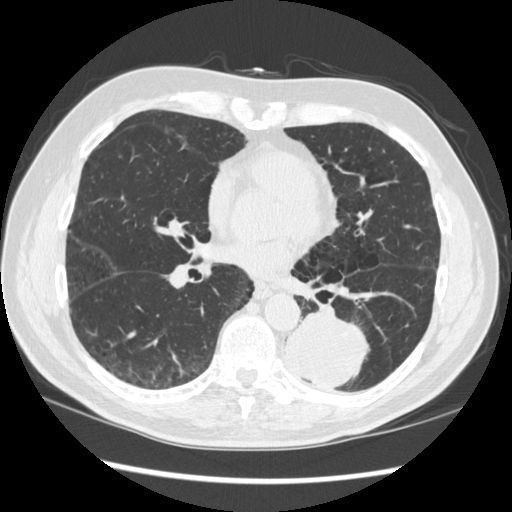
Chest CT (low-dose screening protocol), one axial image; first (baseline) screen; lung window (W 1500 / L -600 HU); 1.25 mm slice thickness; slice 150 of 348 in the series; 512 × 512 image matrix, field of view 360 × 360 mm. Male, age 72 years at enrolment.
• Lesion marked by an expert reader, bounding box (x1, y1, x2, y2) in pixels: (267, 303, 371, 394).
• The screening reader recorded 2 non-calcified nodules or masses ≥4 mm on this exam (left lower lobe, right middle lobe); which of them this box marks is not recorded.
• Official screen result: positive, change unspecified: nodule(s) >= 4 mm or enlarging nodule(s), mass(es), or other non-specific abnormalities suspicious for lung cancer.
• Later outcome: lung cancer diagnosed 37 days after this screen — squamous cell carcinoma, NOS, left lower lobe, stage IIIA (AJCC 6th edition), 60 mm at pathology.